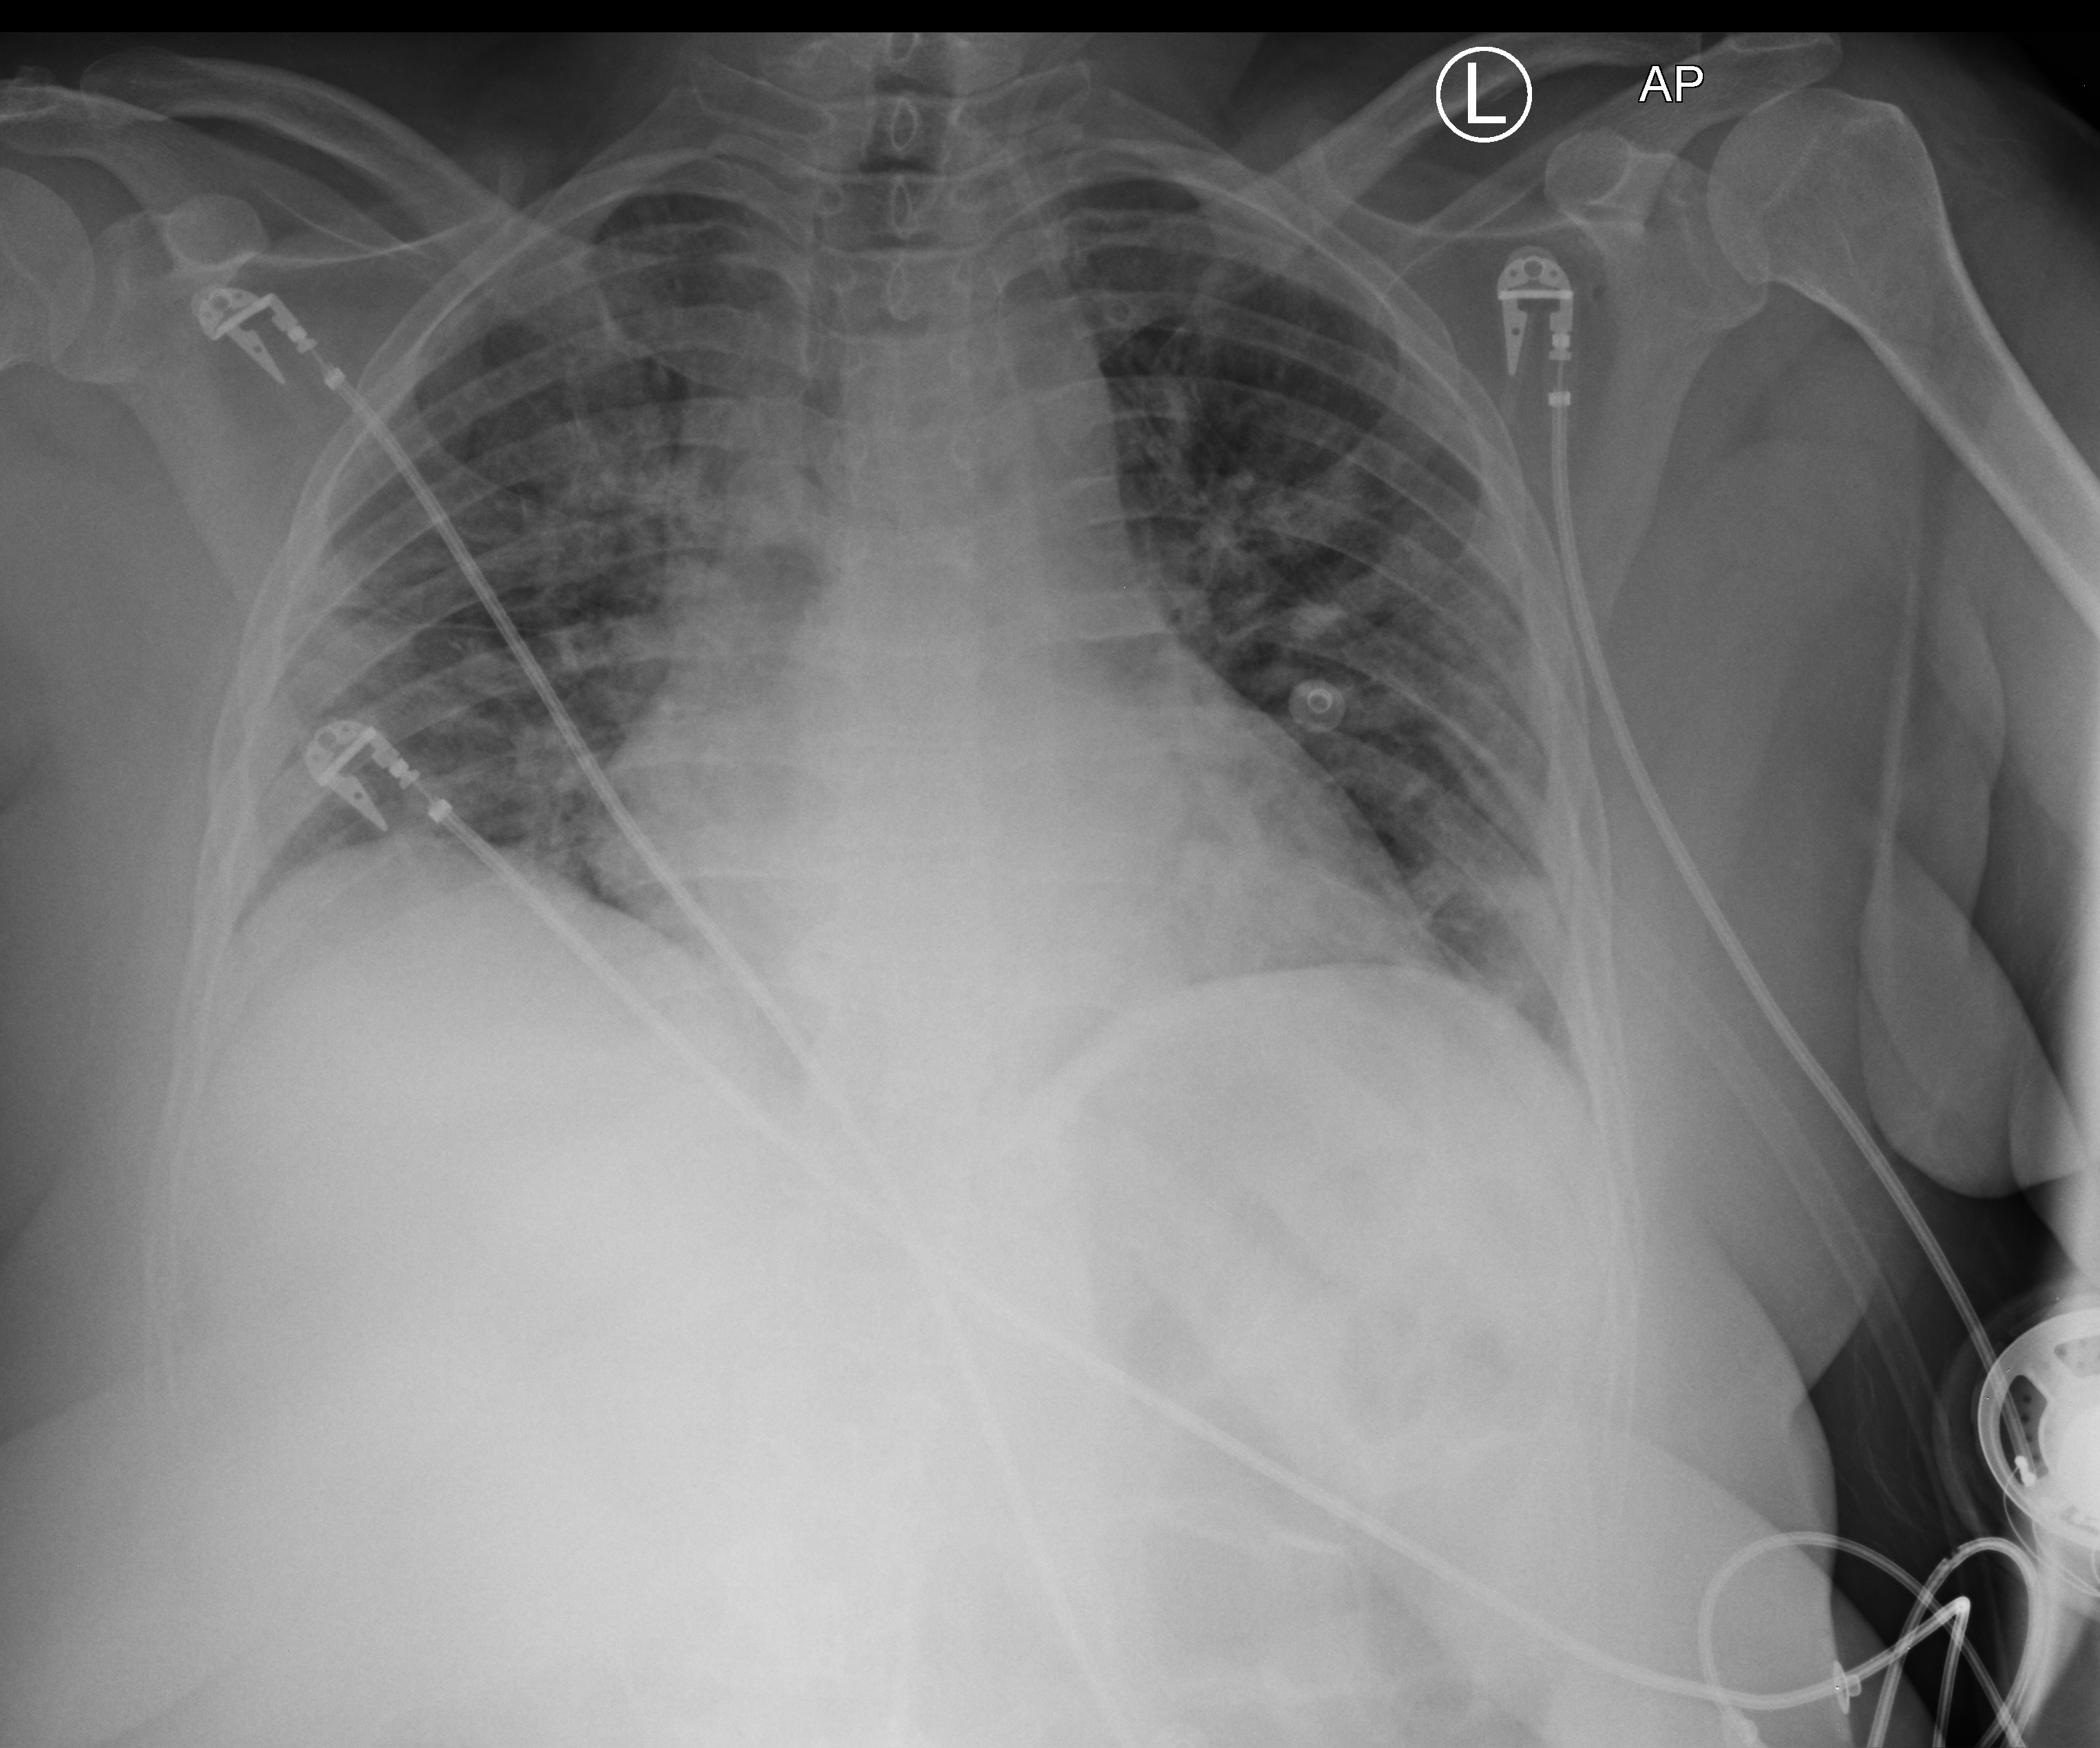
Bedside chest radiograph (computed radiography); anteroposterior (AP) projection. Female patient hospitalised with COVID-19, age 18–59 years.
Hospital-stay facts (about this admission, not read from this image; timing relative to this image not recorded):
- hypertension (admission record): no
- mechanically ventilated during this hospital stay: no
- COPD (admission record): no